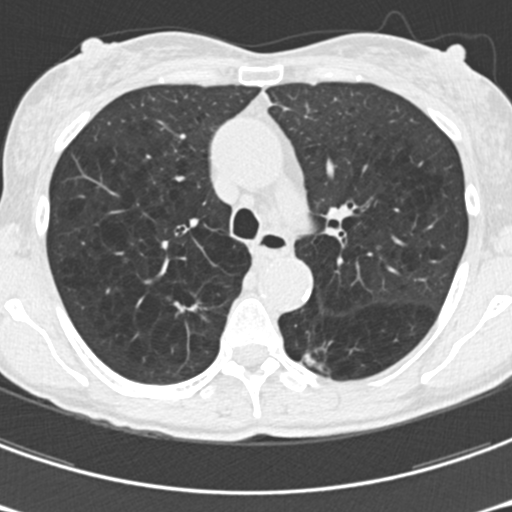
Chest CT (low-dose screening protocol), one axial image. Third screening round (two years after baseline). Lung window (W 1500 / L -600 HU). 2 mm slice thickness. Slice 58 of 176 in the series. 512 × 512 image matrix. Female participant, aged 61 years at enrolment. Current smoker at enrolment.
Lesion marked by an expert reader, bounding box <161,287,216,339> (left, top, right, bottom; pixels). The screening reader recorded 2 non-calcified nodules or masses ≥4 mm on this exam (right upper lobe, right upper lobe); which of them this box marks is not recorded. Official screen result: positive, other. Lung cancer was diagnosed 77 days after this screen: non-small cell carcinoma, right upper lobe, undifferentiated (G4), stage IA (AJCC 6th edition), 15 mm at pathology.